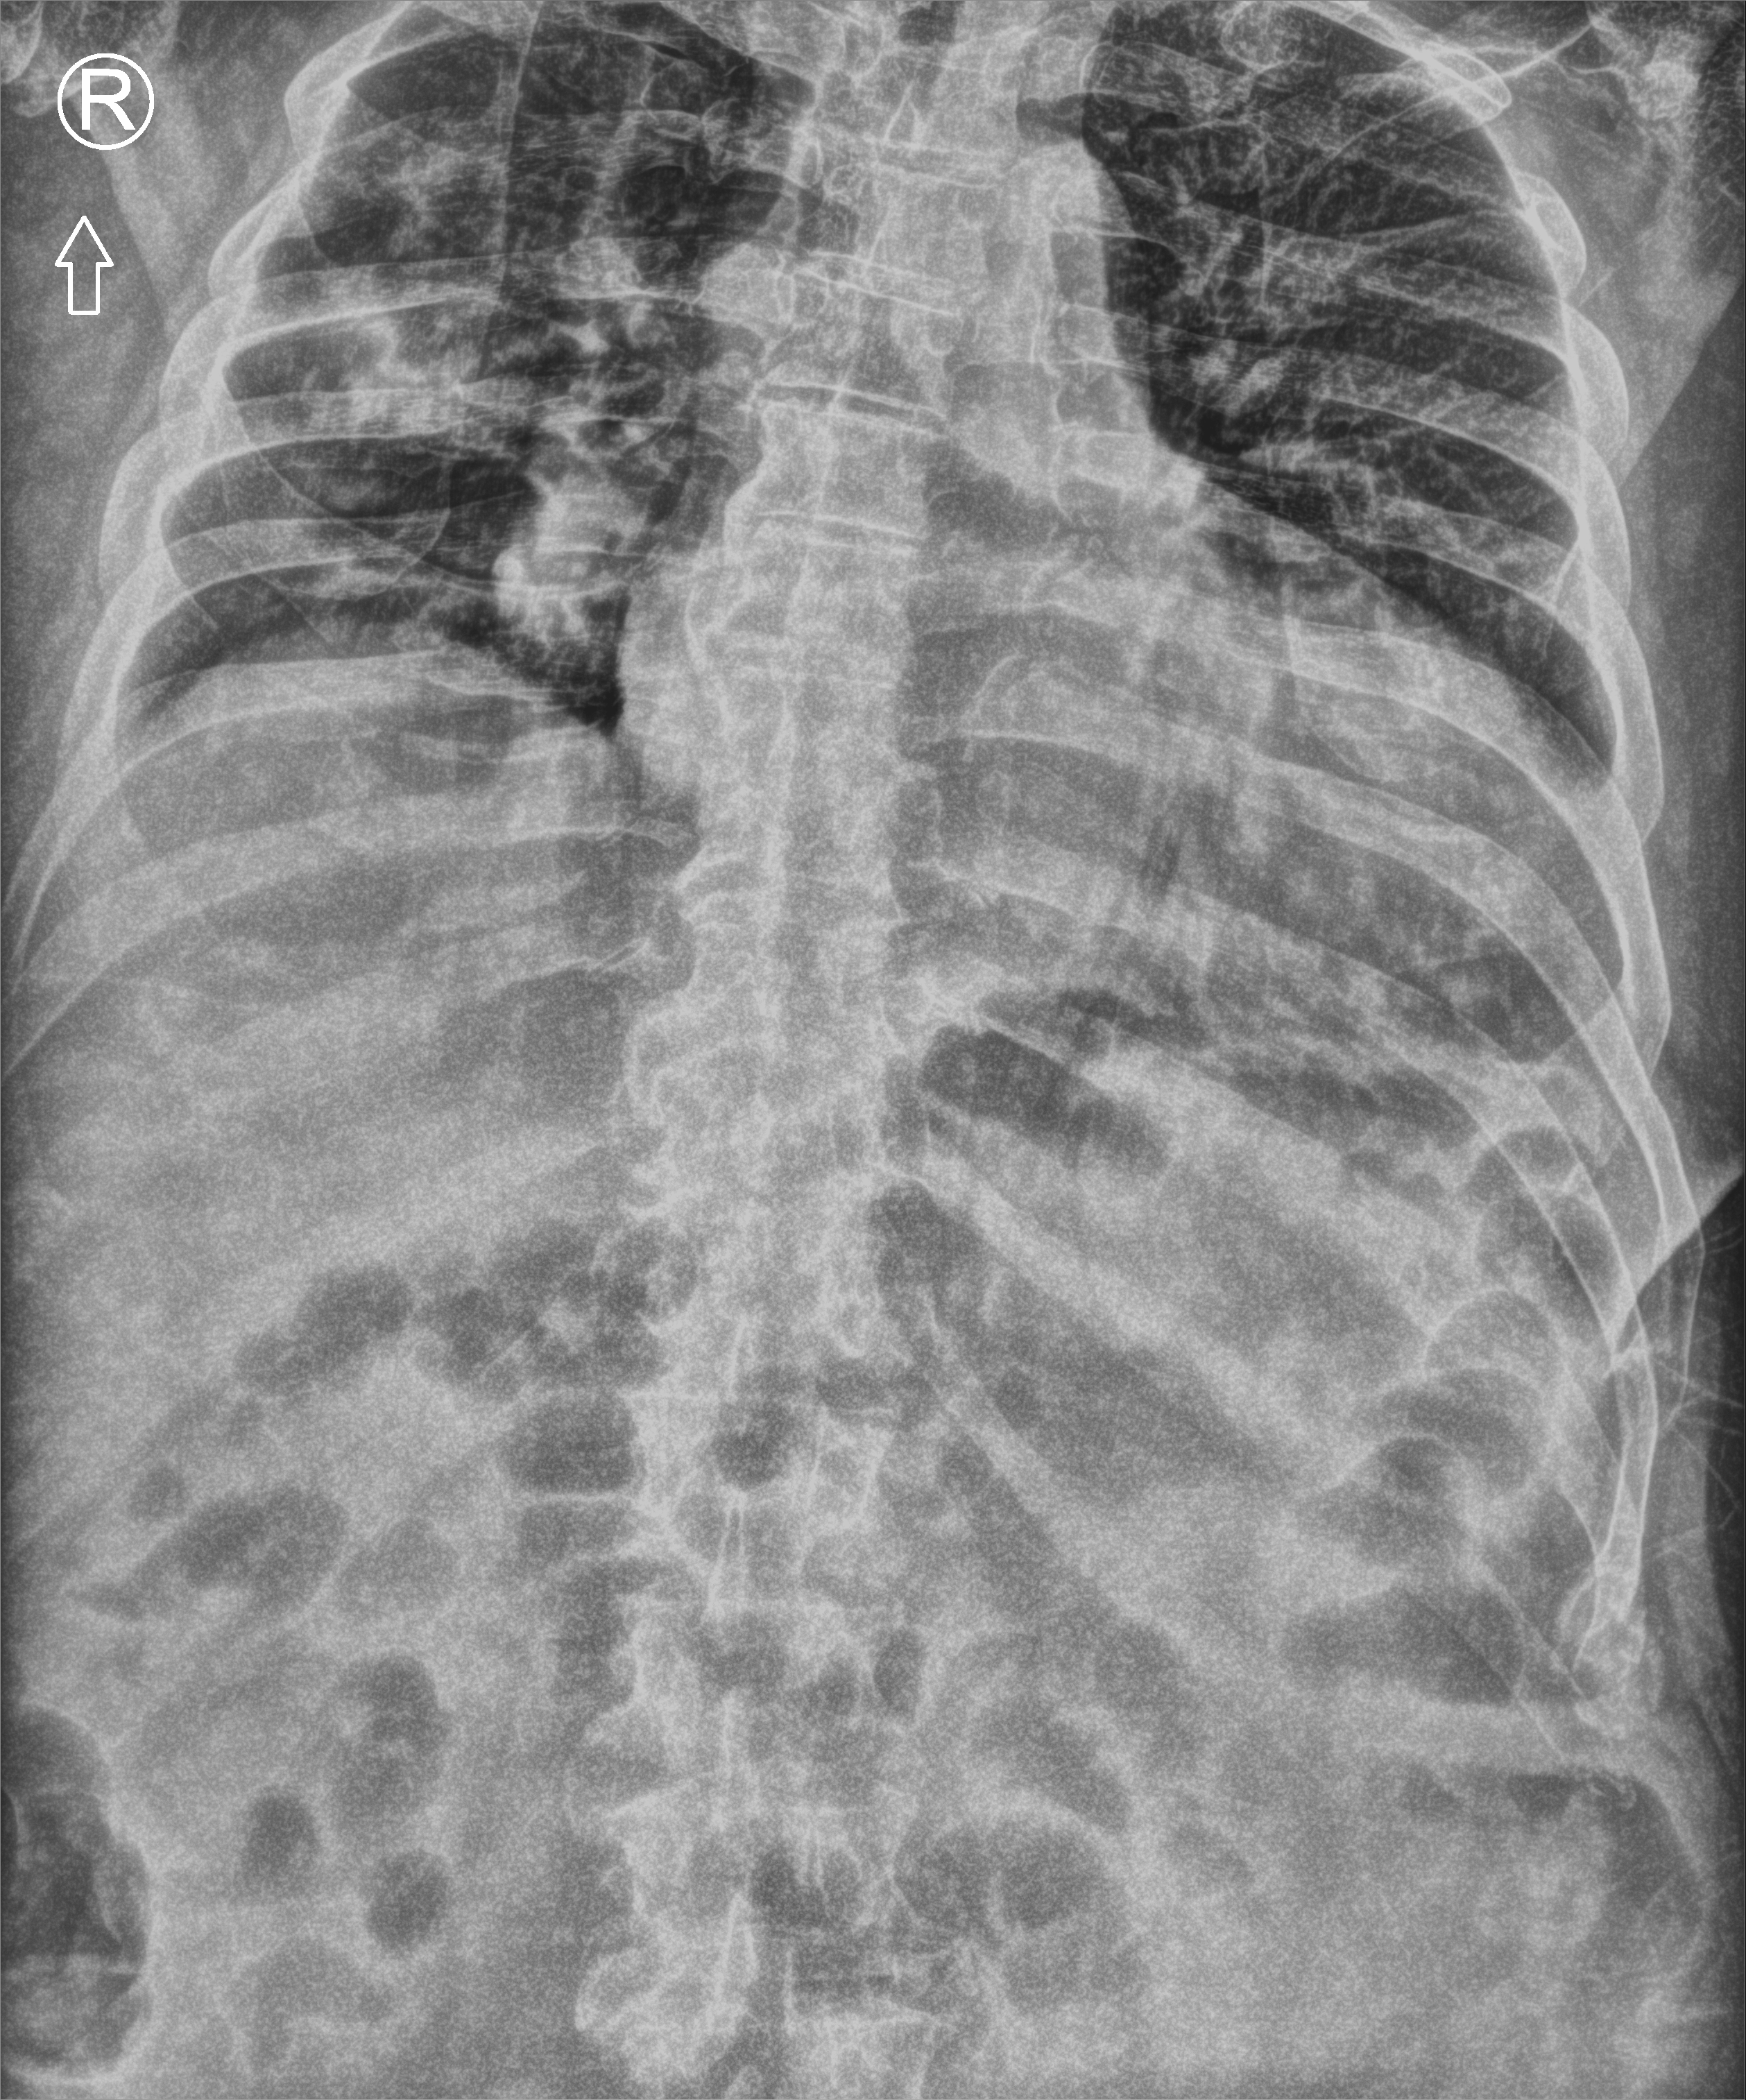
Abdomen X-ray (portable); anteroposterior (AP) projection. Patient hospitalised with COVID-19; male, aged 75–90 years.
Admission-level facts for this patient (not findings on this image; timing relative to this image not recorded): diabetes (admission record): no; other chronic lung disease (admission record): no; admitted to intensive care during this hospital stay: no.